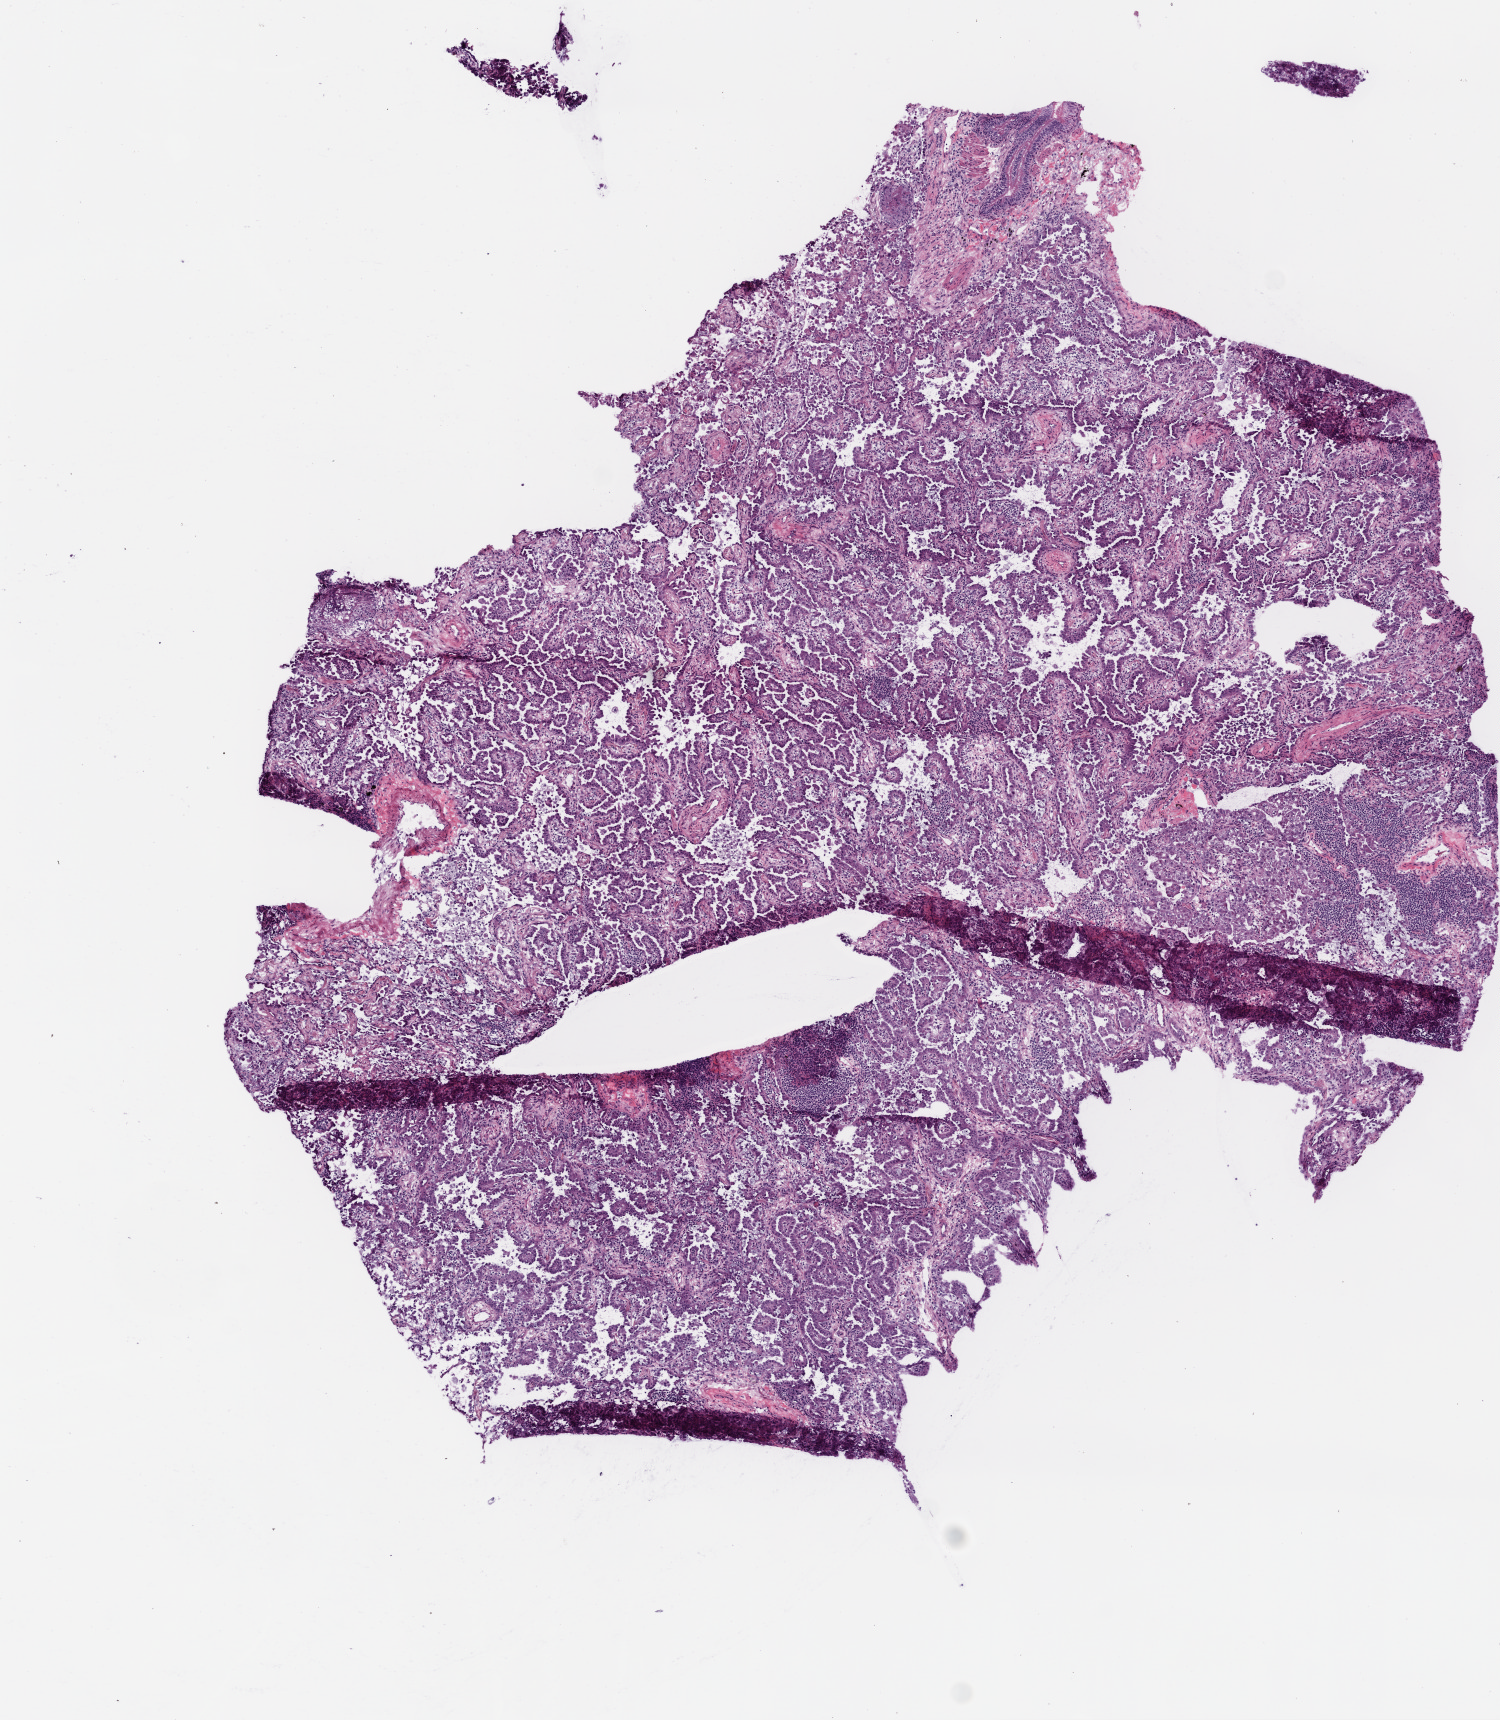
Hematoxylin and eosin (H&E) stained whole-slide image, a low-resolution overview of the entire scanned area, about 6.0 x 6.9 mm (acquisition: 20x scan); frozen section; sample: primary tumour, lung. Patient: female, age at initial diagnosis 73 years. Composition of this section per pathologist review: tumour cells 94%, tumour nuclei 80%, normal cells 1%, stromal cells 5%, necrosis 0%.
TNM: T2 N0 M0. AJCC pathologic stage: IB (6th edition). Pathologic diagnosis: Adenocarcinoma, NOS (lower lobe, lung).